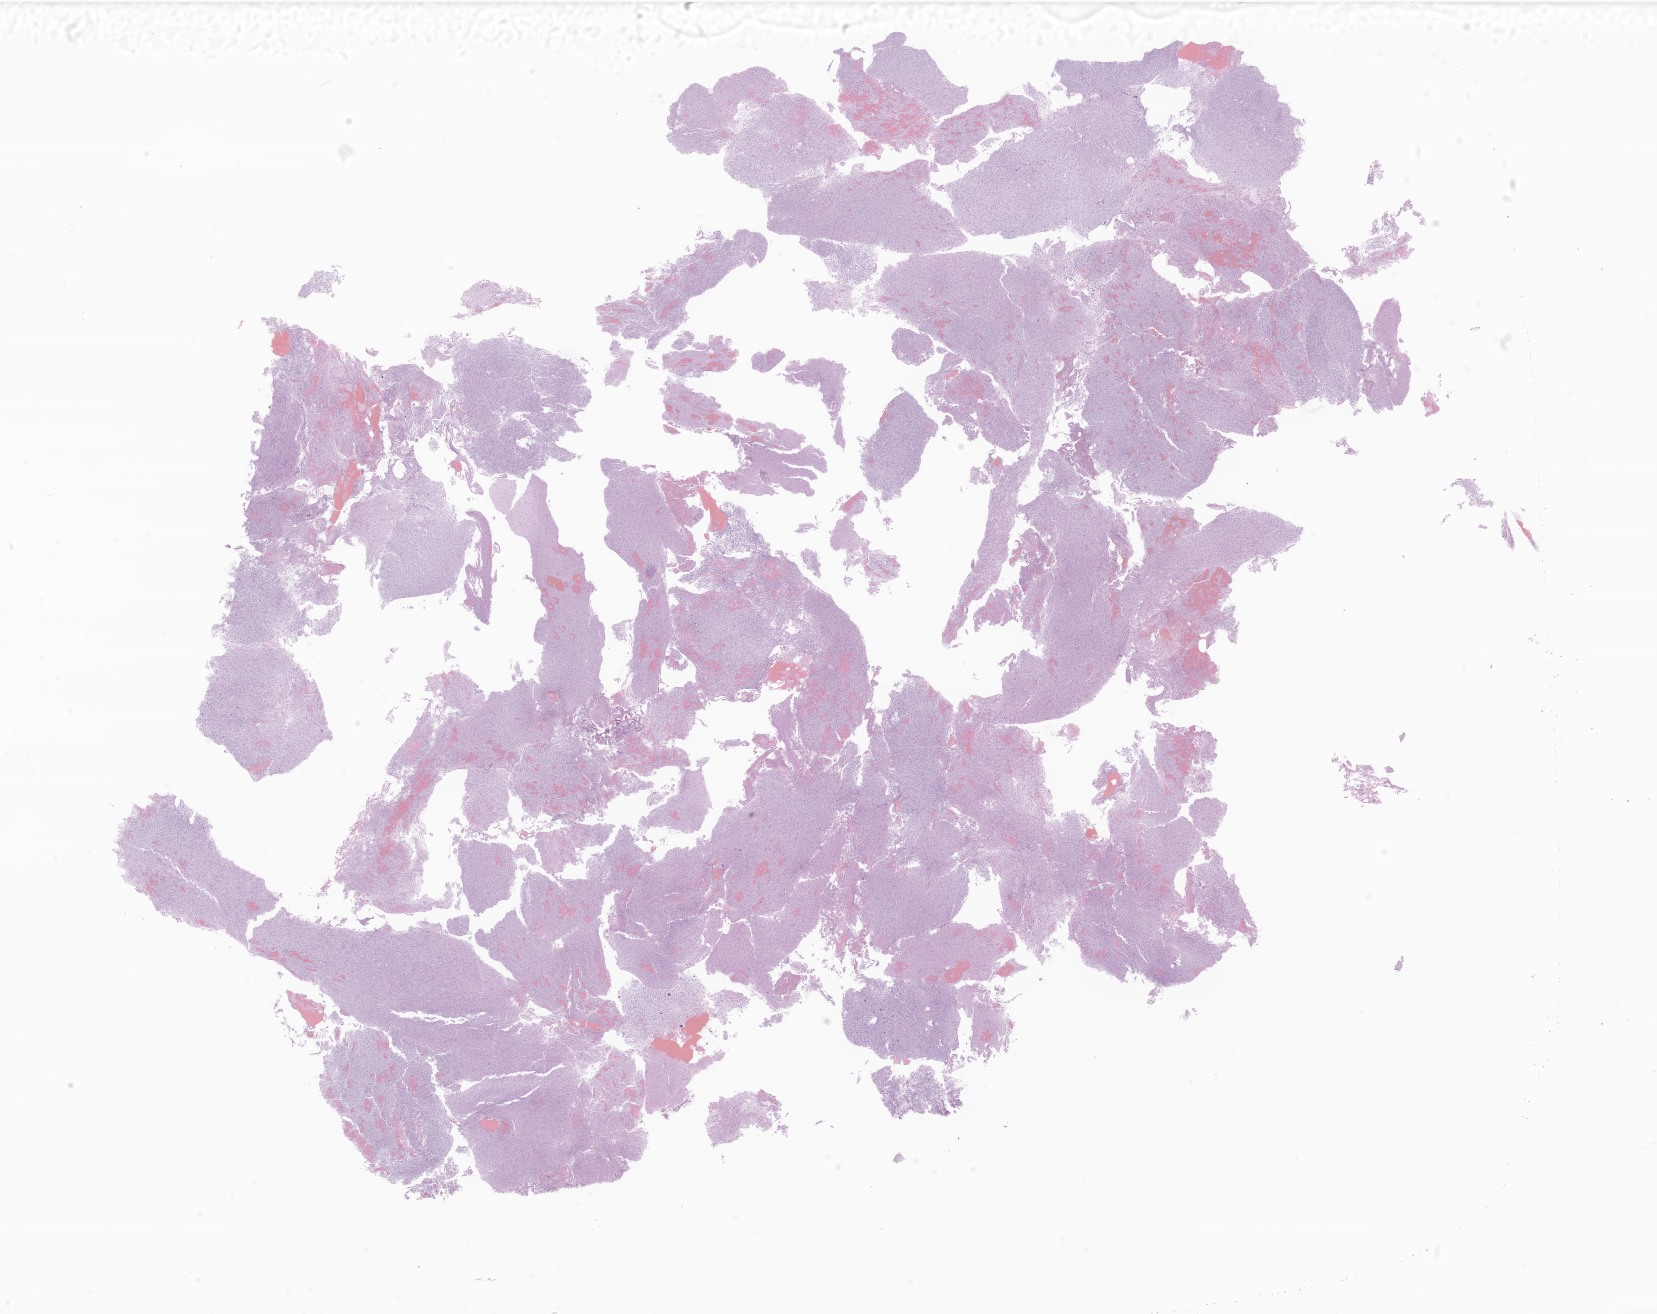
Hematoxylin and eosin (H&E) whole-slide image of tumor tissue from the brain, shown as a low-resolution overview of the whole scanned area (about 27.9 x 22.2 mm). Formalin-fixed, paraffin-embedded (FFPE) tissue. Male patient, age 196 months (16 years 4 months).
* diagnosis: Tumor cells, malignant